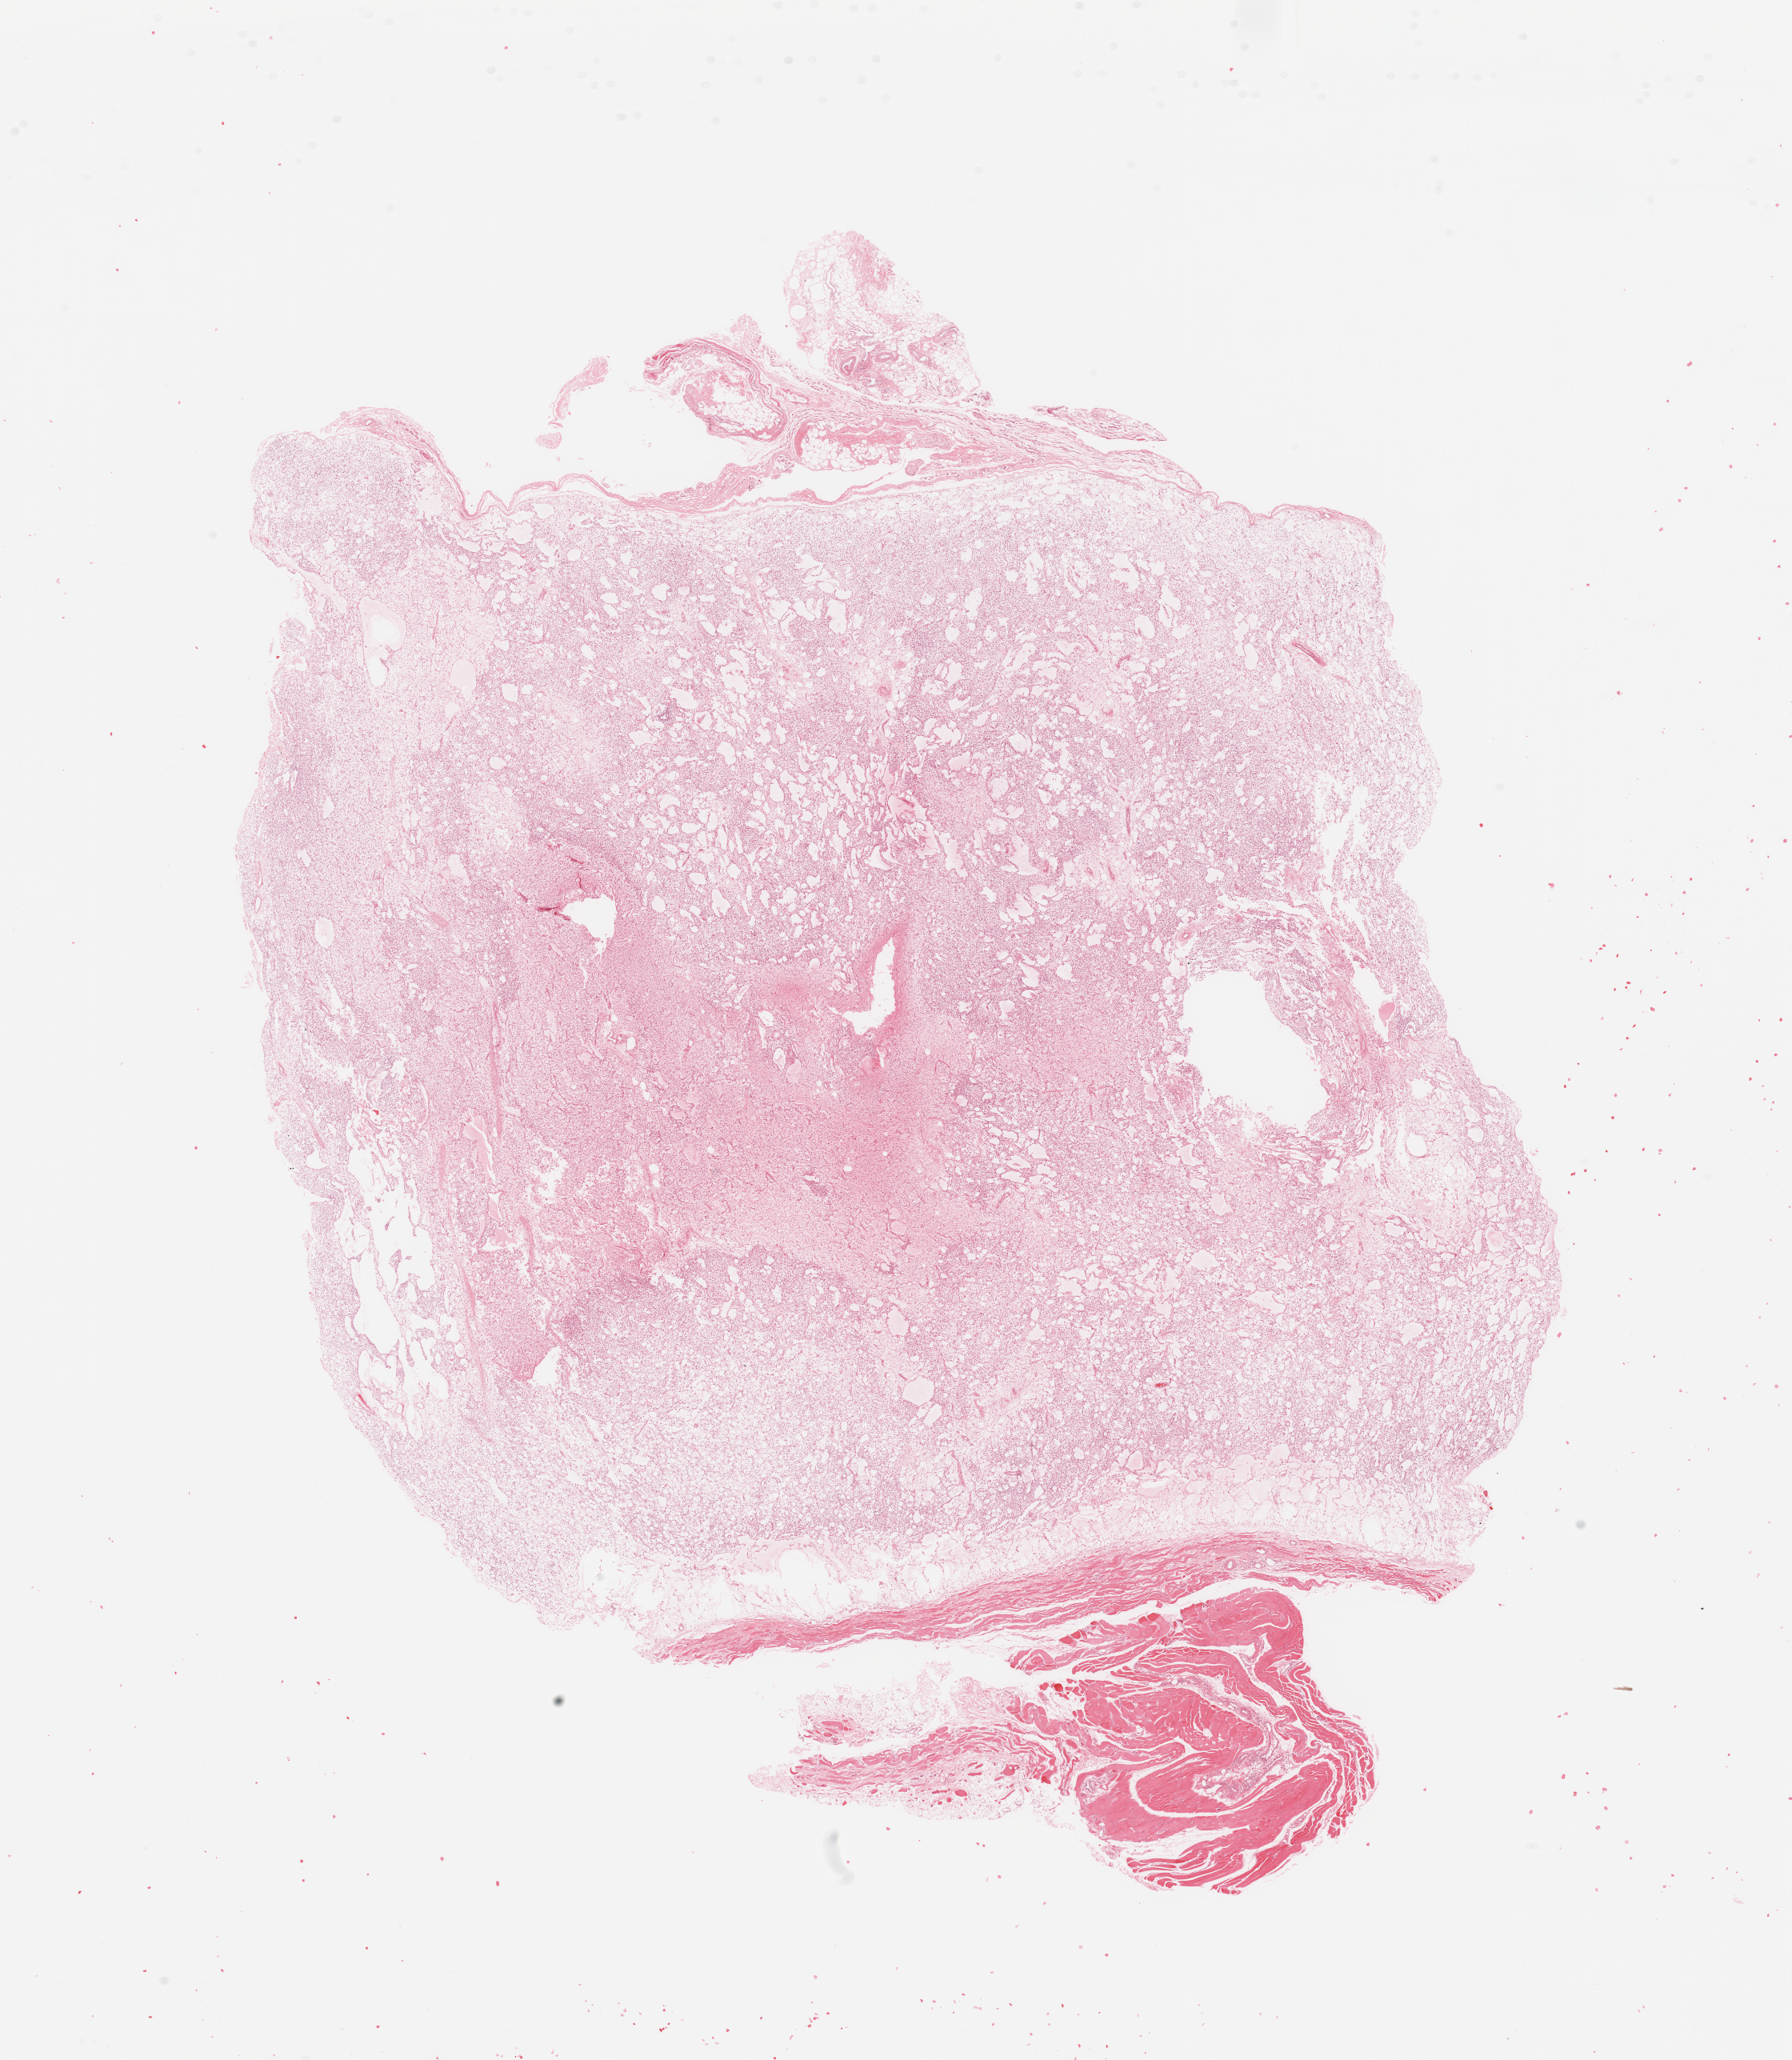
H&E-stained whole-slide image, a low-resolution overview of the entire scanned area, about 17.7 x 20.4 mm (from a 20x scan). Tumour tissue sample. 32-year-old female patient.
Patient diagnosis (cohort enrolment): sarcoma (site not recorded at cohort level).